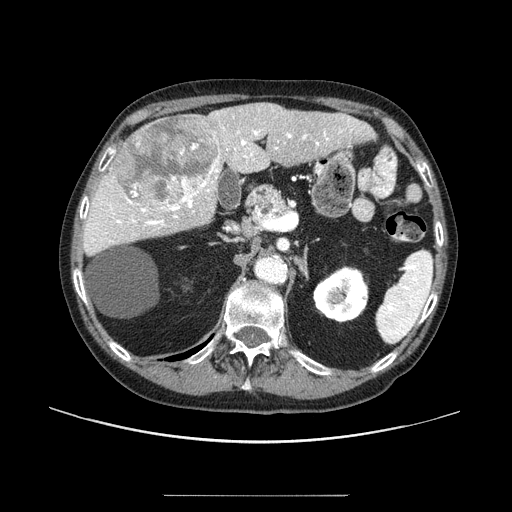
Contrast-enhanced abdominal CT (liver protocol), one axial slice; position 50 of 91 along the scan axis; reconstruction kernel STANDARD; 100 kVp; one of 2 acquisitions stored at this slice position; soft-tissue window (W 400 / L 40 HU); 2.5 mm slice thickness; 512 × 512 image matrix, field of view 400 × 400 mm. From the clinical record (not read from this slice): diagnosis: hepatocellular carcinoma (patient treated with transarterial chemoembolisation; whether this scan precedes or follows treatment is not stated here); TNM stage (as recorded): Stage-I; Child-Pugh class: A; tumour differentiation: moderately differentiated; tumour nodularity: uninodular.
Outlined on this slice (semi-automatically segmented with operator editing):
- liver parenchyma outside the tumour (the mass and vessels are separate outlines, so this box may not span the whole liver): bounding box <82,102,374,256> (left, top, right, bottom; pixels)
- mass: <111,114,220,210>
- liver vessels: <85,127,352,246>